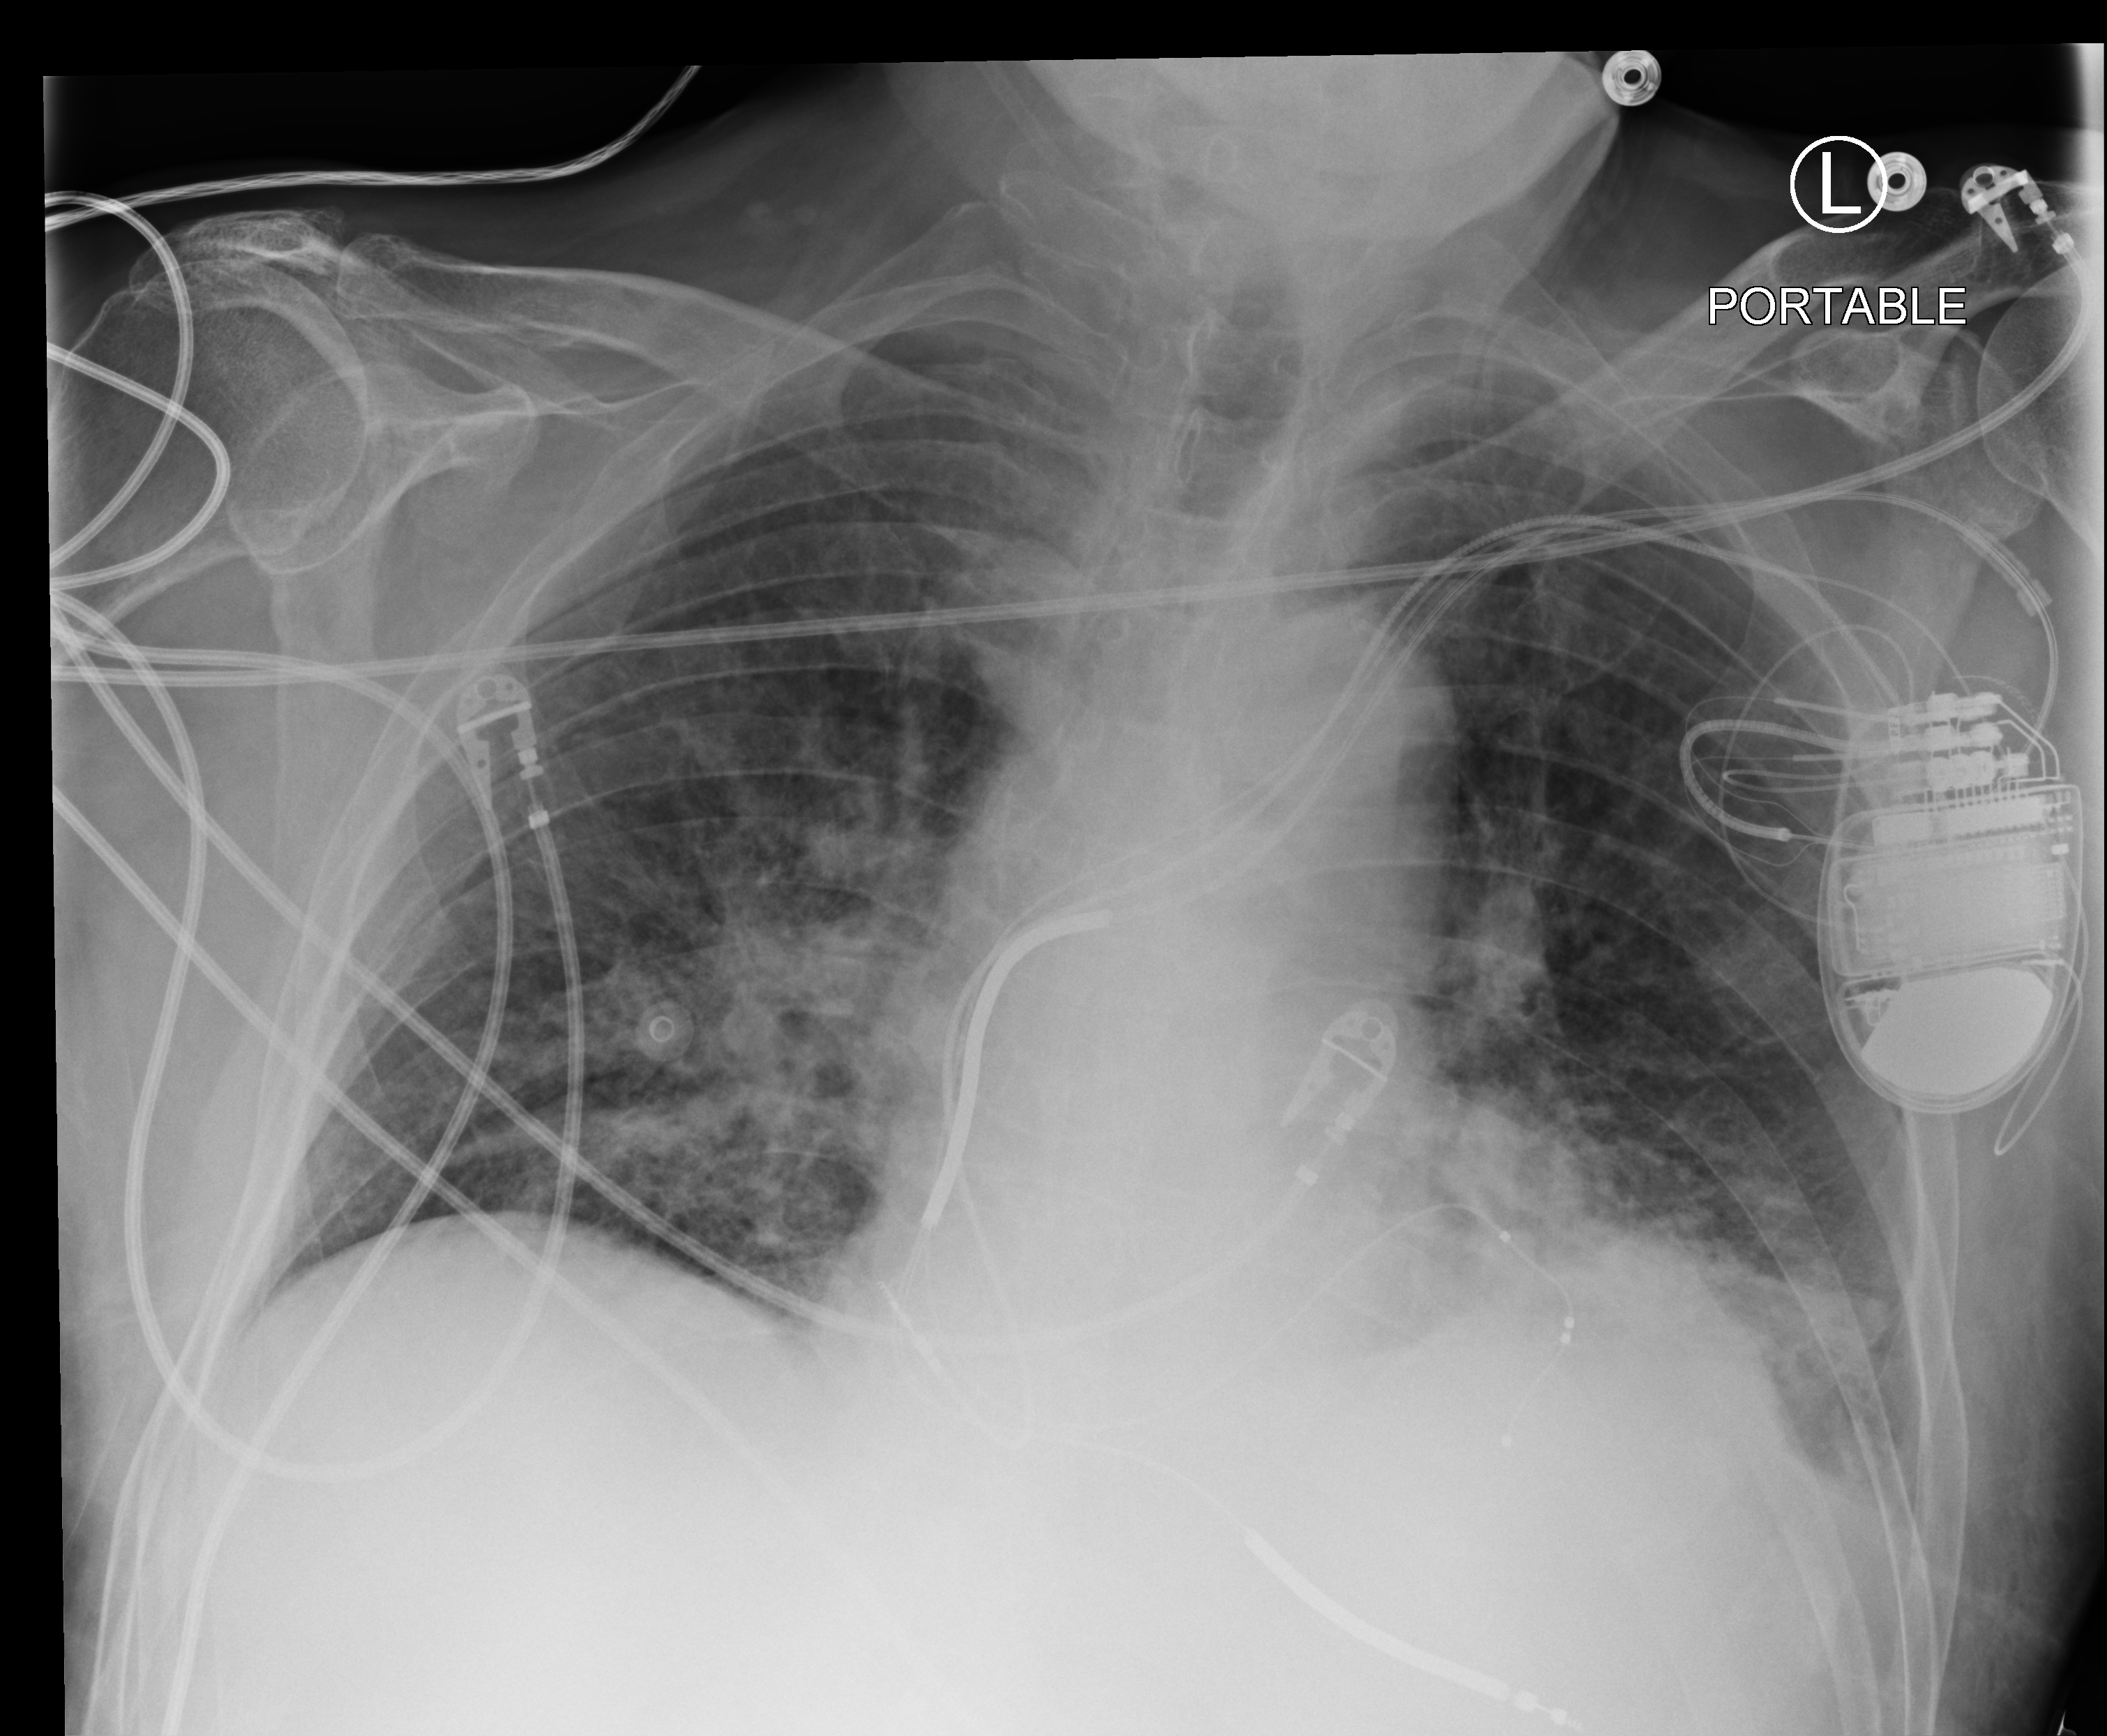
Bedside chest radiograph (computed radiography); anteroposterior (AP) projection. Patient hospitalised with COVID-19; male, aged 75–90 years.
Admission-level facts for this patient (not findings on this image; timing relative to this image not recorded):
- admitted to intensive care during this hospital stay: no
- mechanically ventilated during this hospital stay: no